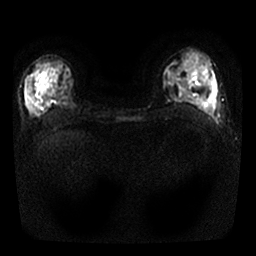
Breast MRI, one axial slice; slice 13 of 25 in the series (ordered by position); diffusion-weighted series; image 2 of 4 stored at this slice position (different b-values; order by instance number); 1.5 T; 256 × 256 image matrix. Female patient.
Outlined on this slice (outlined manually by an expert reader):
- tumour on diffusion-weighted imaging: bounding box (x1, y1, x2, y2) in pixels: (26, 96, 31, 111)